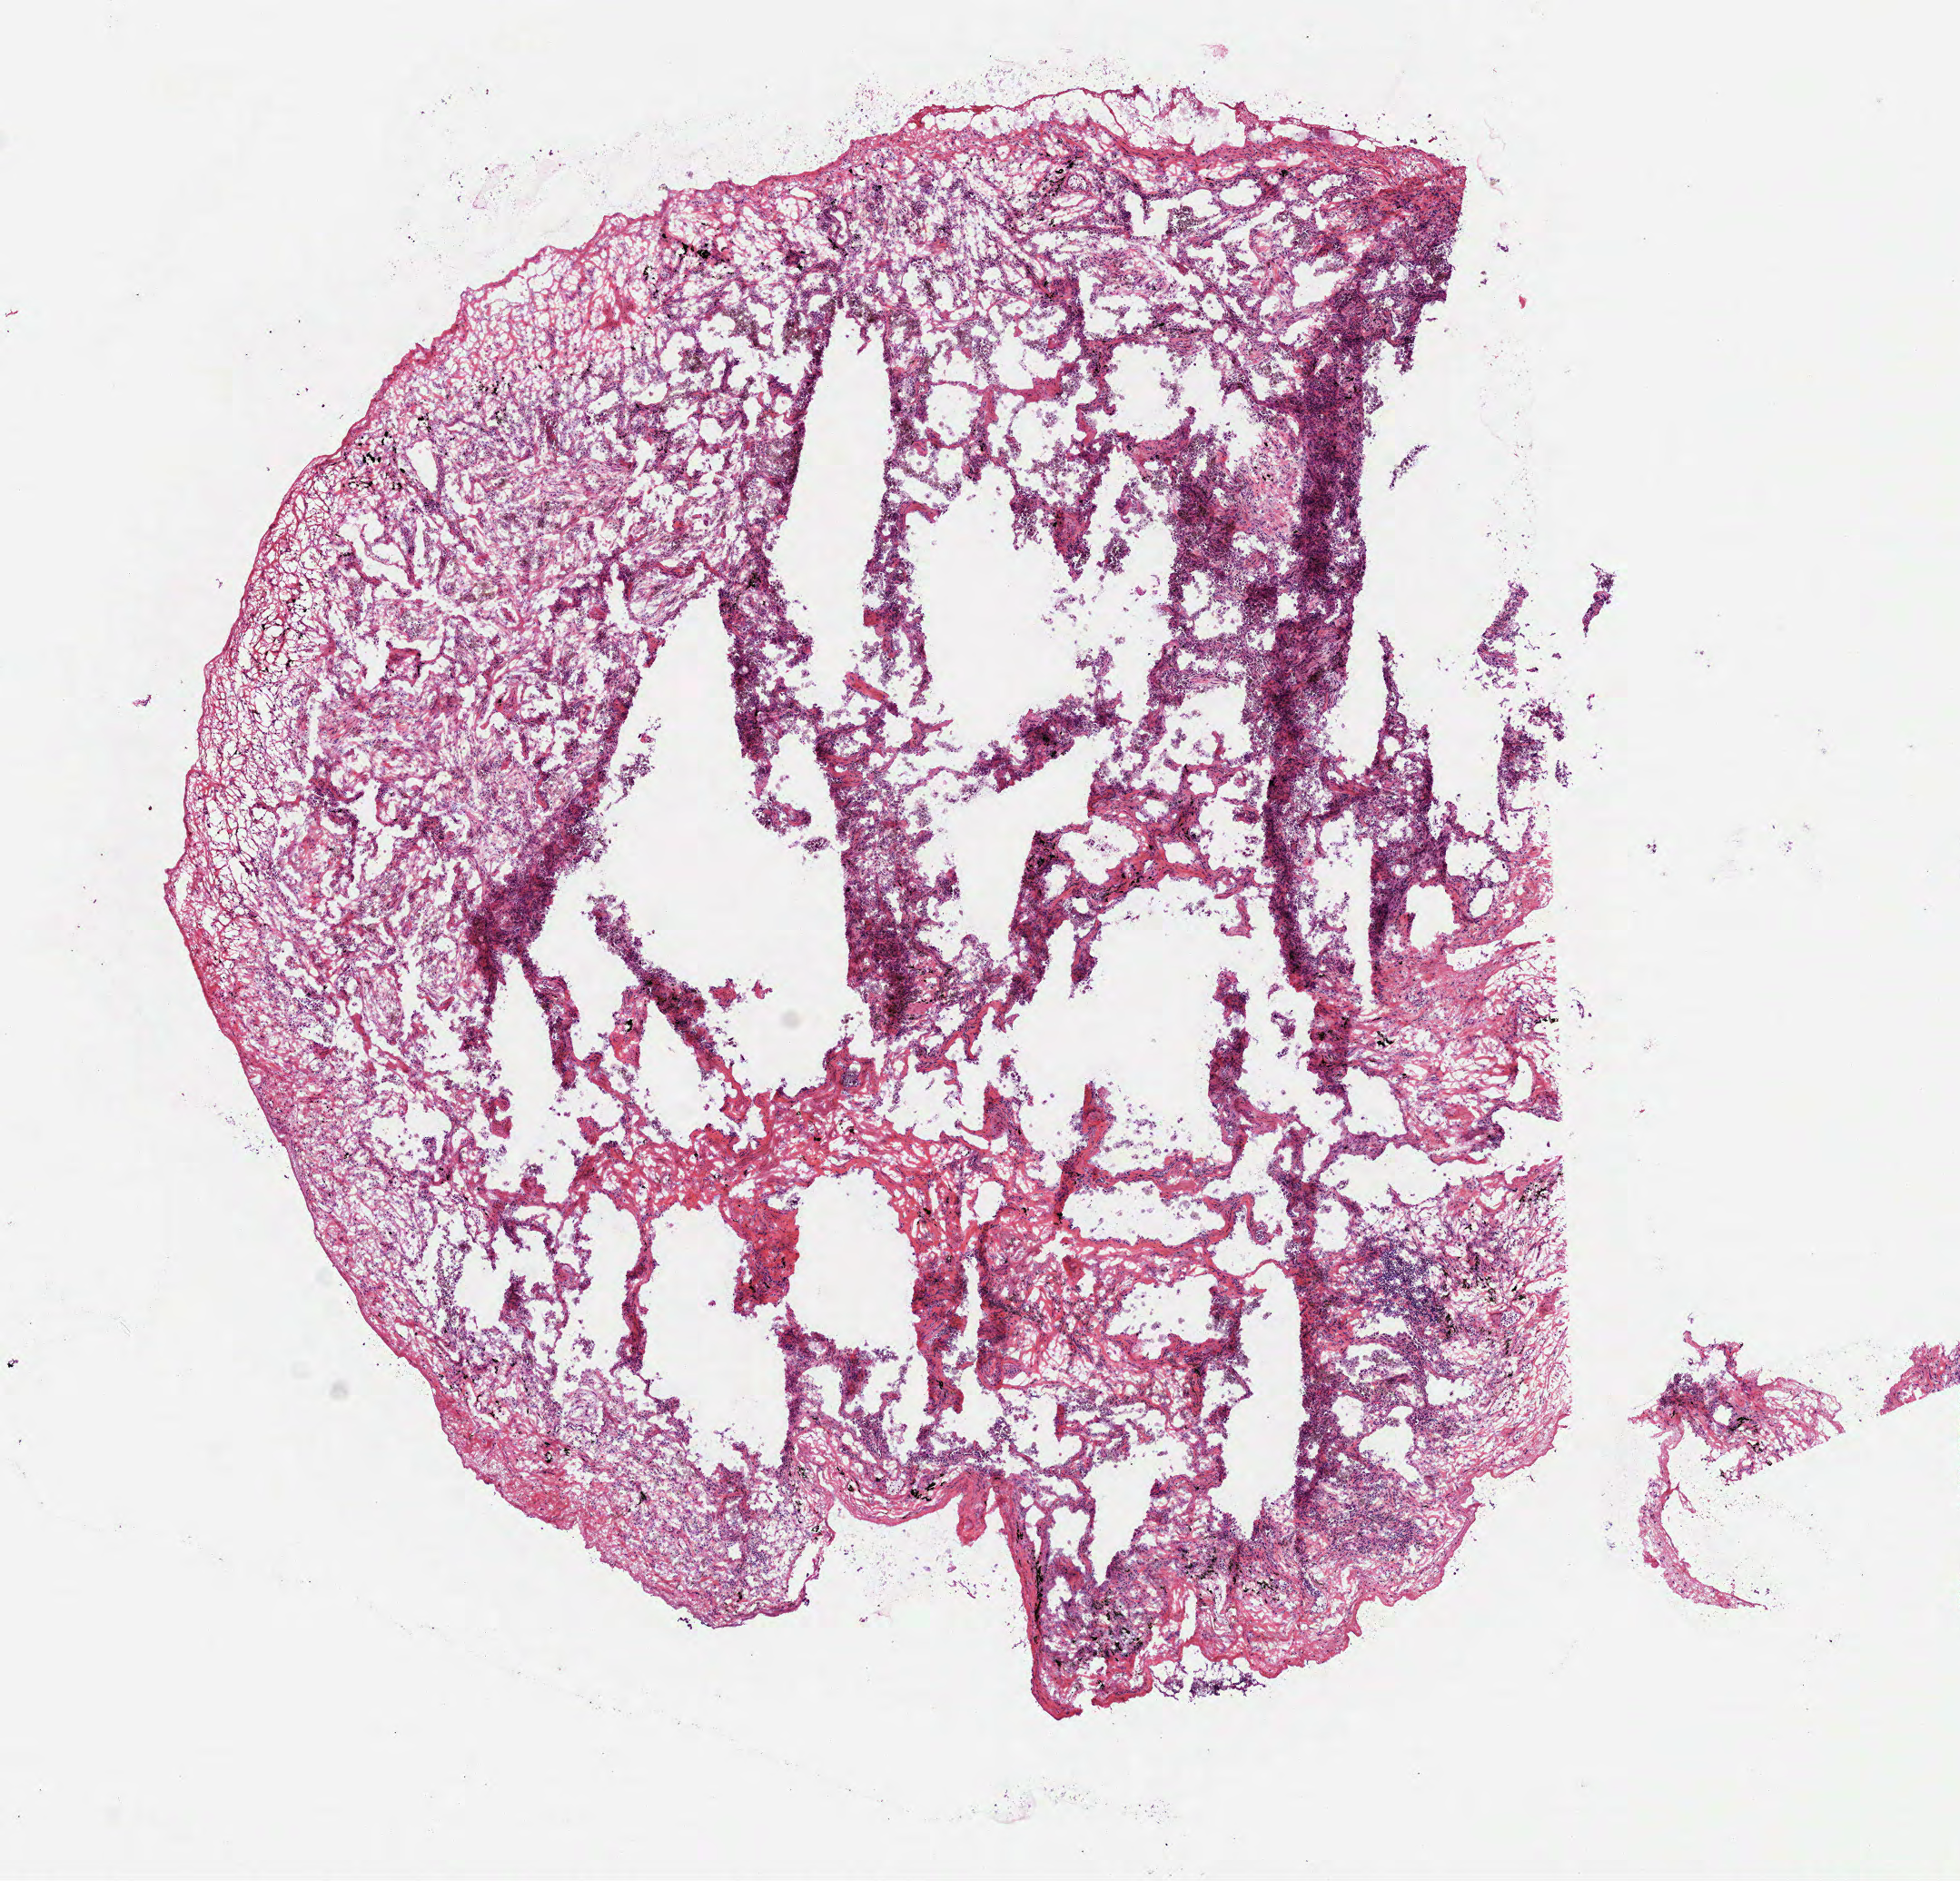
Digitized H&E tissue section (whole slide) — shown as a low-resolution overview of the whole scanned area (about 8.7 x 8.4 mm, acquisition: 40x scan). Frozen section from the top of the tissue portion. Sample: solid tissue normal (non-tumour tissue), lung. Male patient; age at initial diagnosis 70 years.
- this section: solid tissue normal sample (biorepository sample class)
- patient diagnosis: Squamous cell carcinoma, NOS (lower lobe, lung)